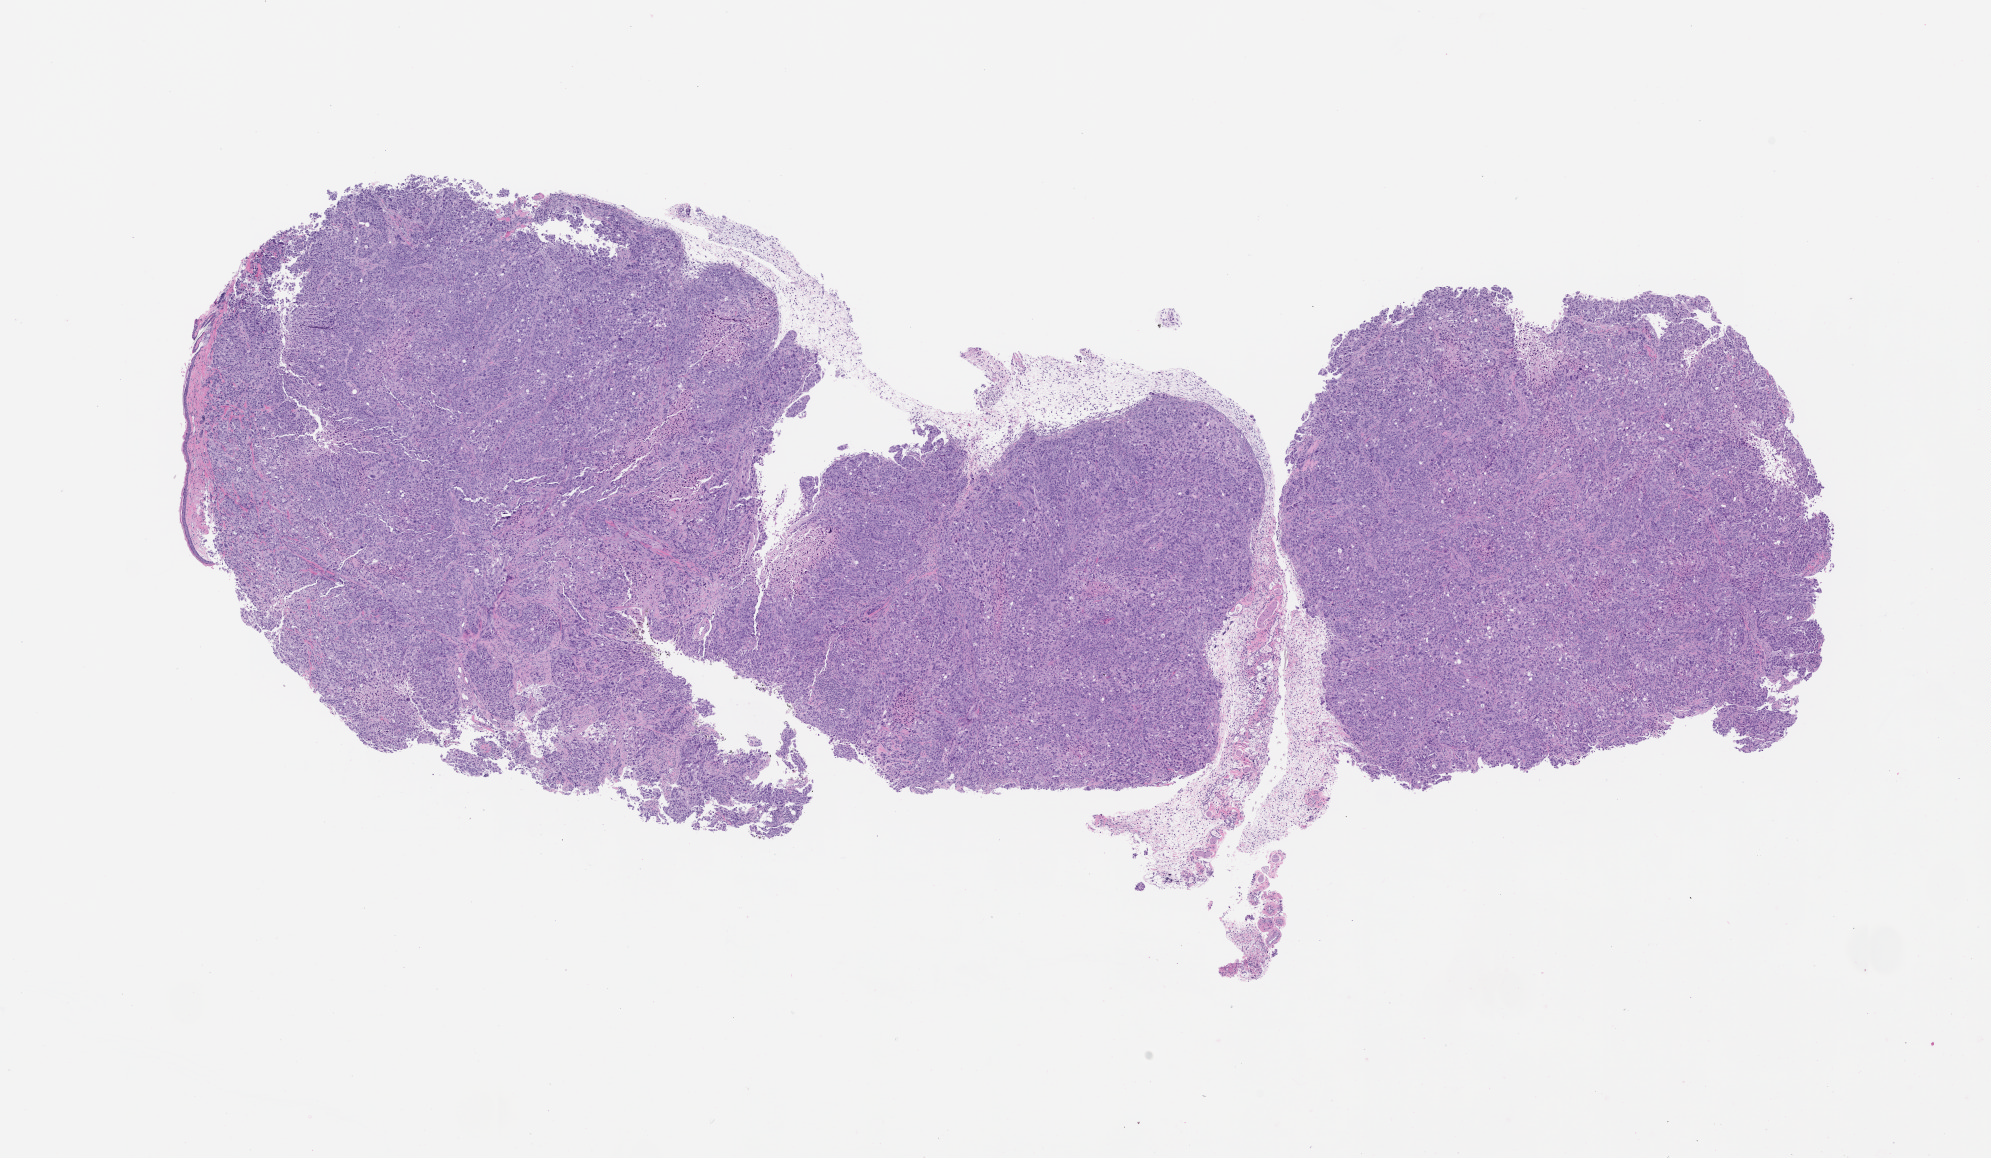
Whole-slide image, haematoxylin and eosin: patient-derived xenograft (human tumor grown in a mouse), passage 2 — shown as a low-resolution overview of the whole scanned area (about 16.0 x 9.3 mm), formalin-fixed paraffin-embedded section, originating tumor site category: lung.
- originating patient diagnosis: Lung Adenocarcinoma